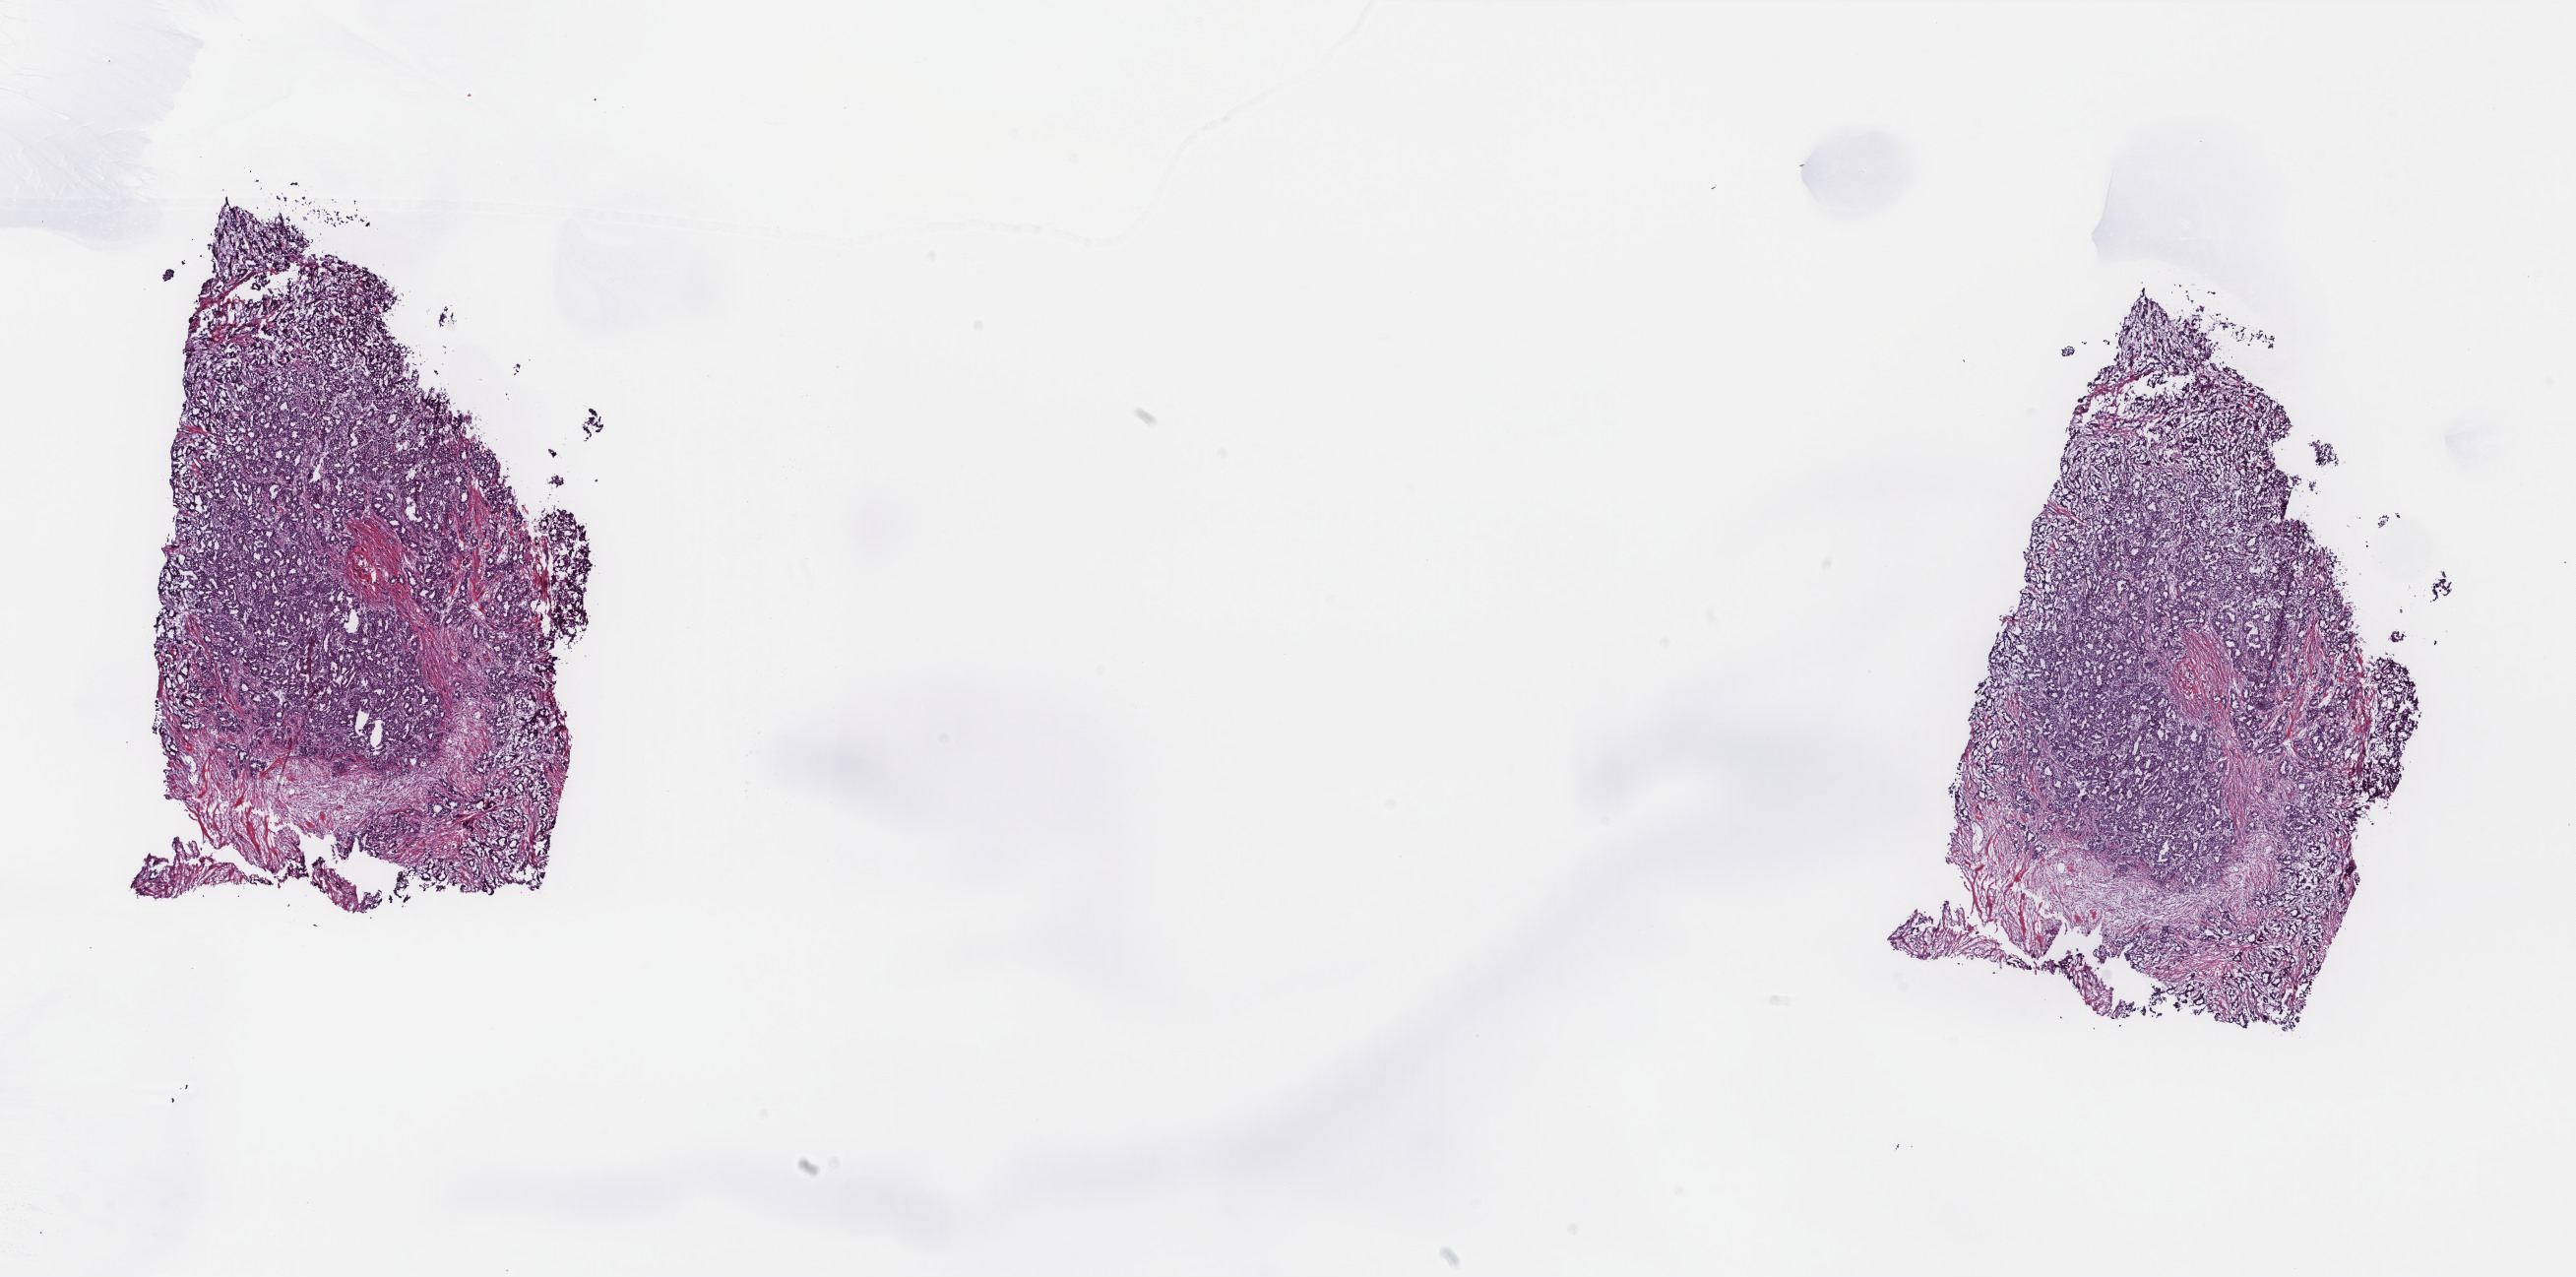
H&E whole-slide image — low-resolution overview of the scanned area, about 20.8 x 10.3 mm (slide scanned at 40x). Frozen section from the top of the tissue portion. Sample: primary tumour, breast. Female patient; age at initial diagnosis 62 years. Pathologist review of this section (percent, as recorded): tumour cells 100%, tumour nuclei 90%, normal cells 0%, stromal cells 0%, necrosis 0%. Infiltration values recorded for this section: lymphocyte infiltration 0%, monocyte infiltration 0%, neutrophil infiltration 0%.
AJCC pathologic stage: IIA (7th edition). Lymph nodes positive (case pathology): 3 of 10 examined. TNM: T1c N1a M0. Pathologic diagnosis: Infiltrating duct carcinoma, NOS.